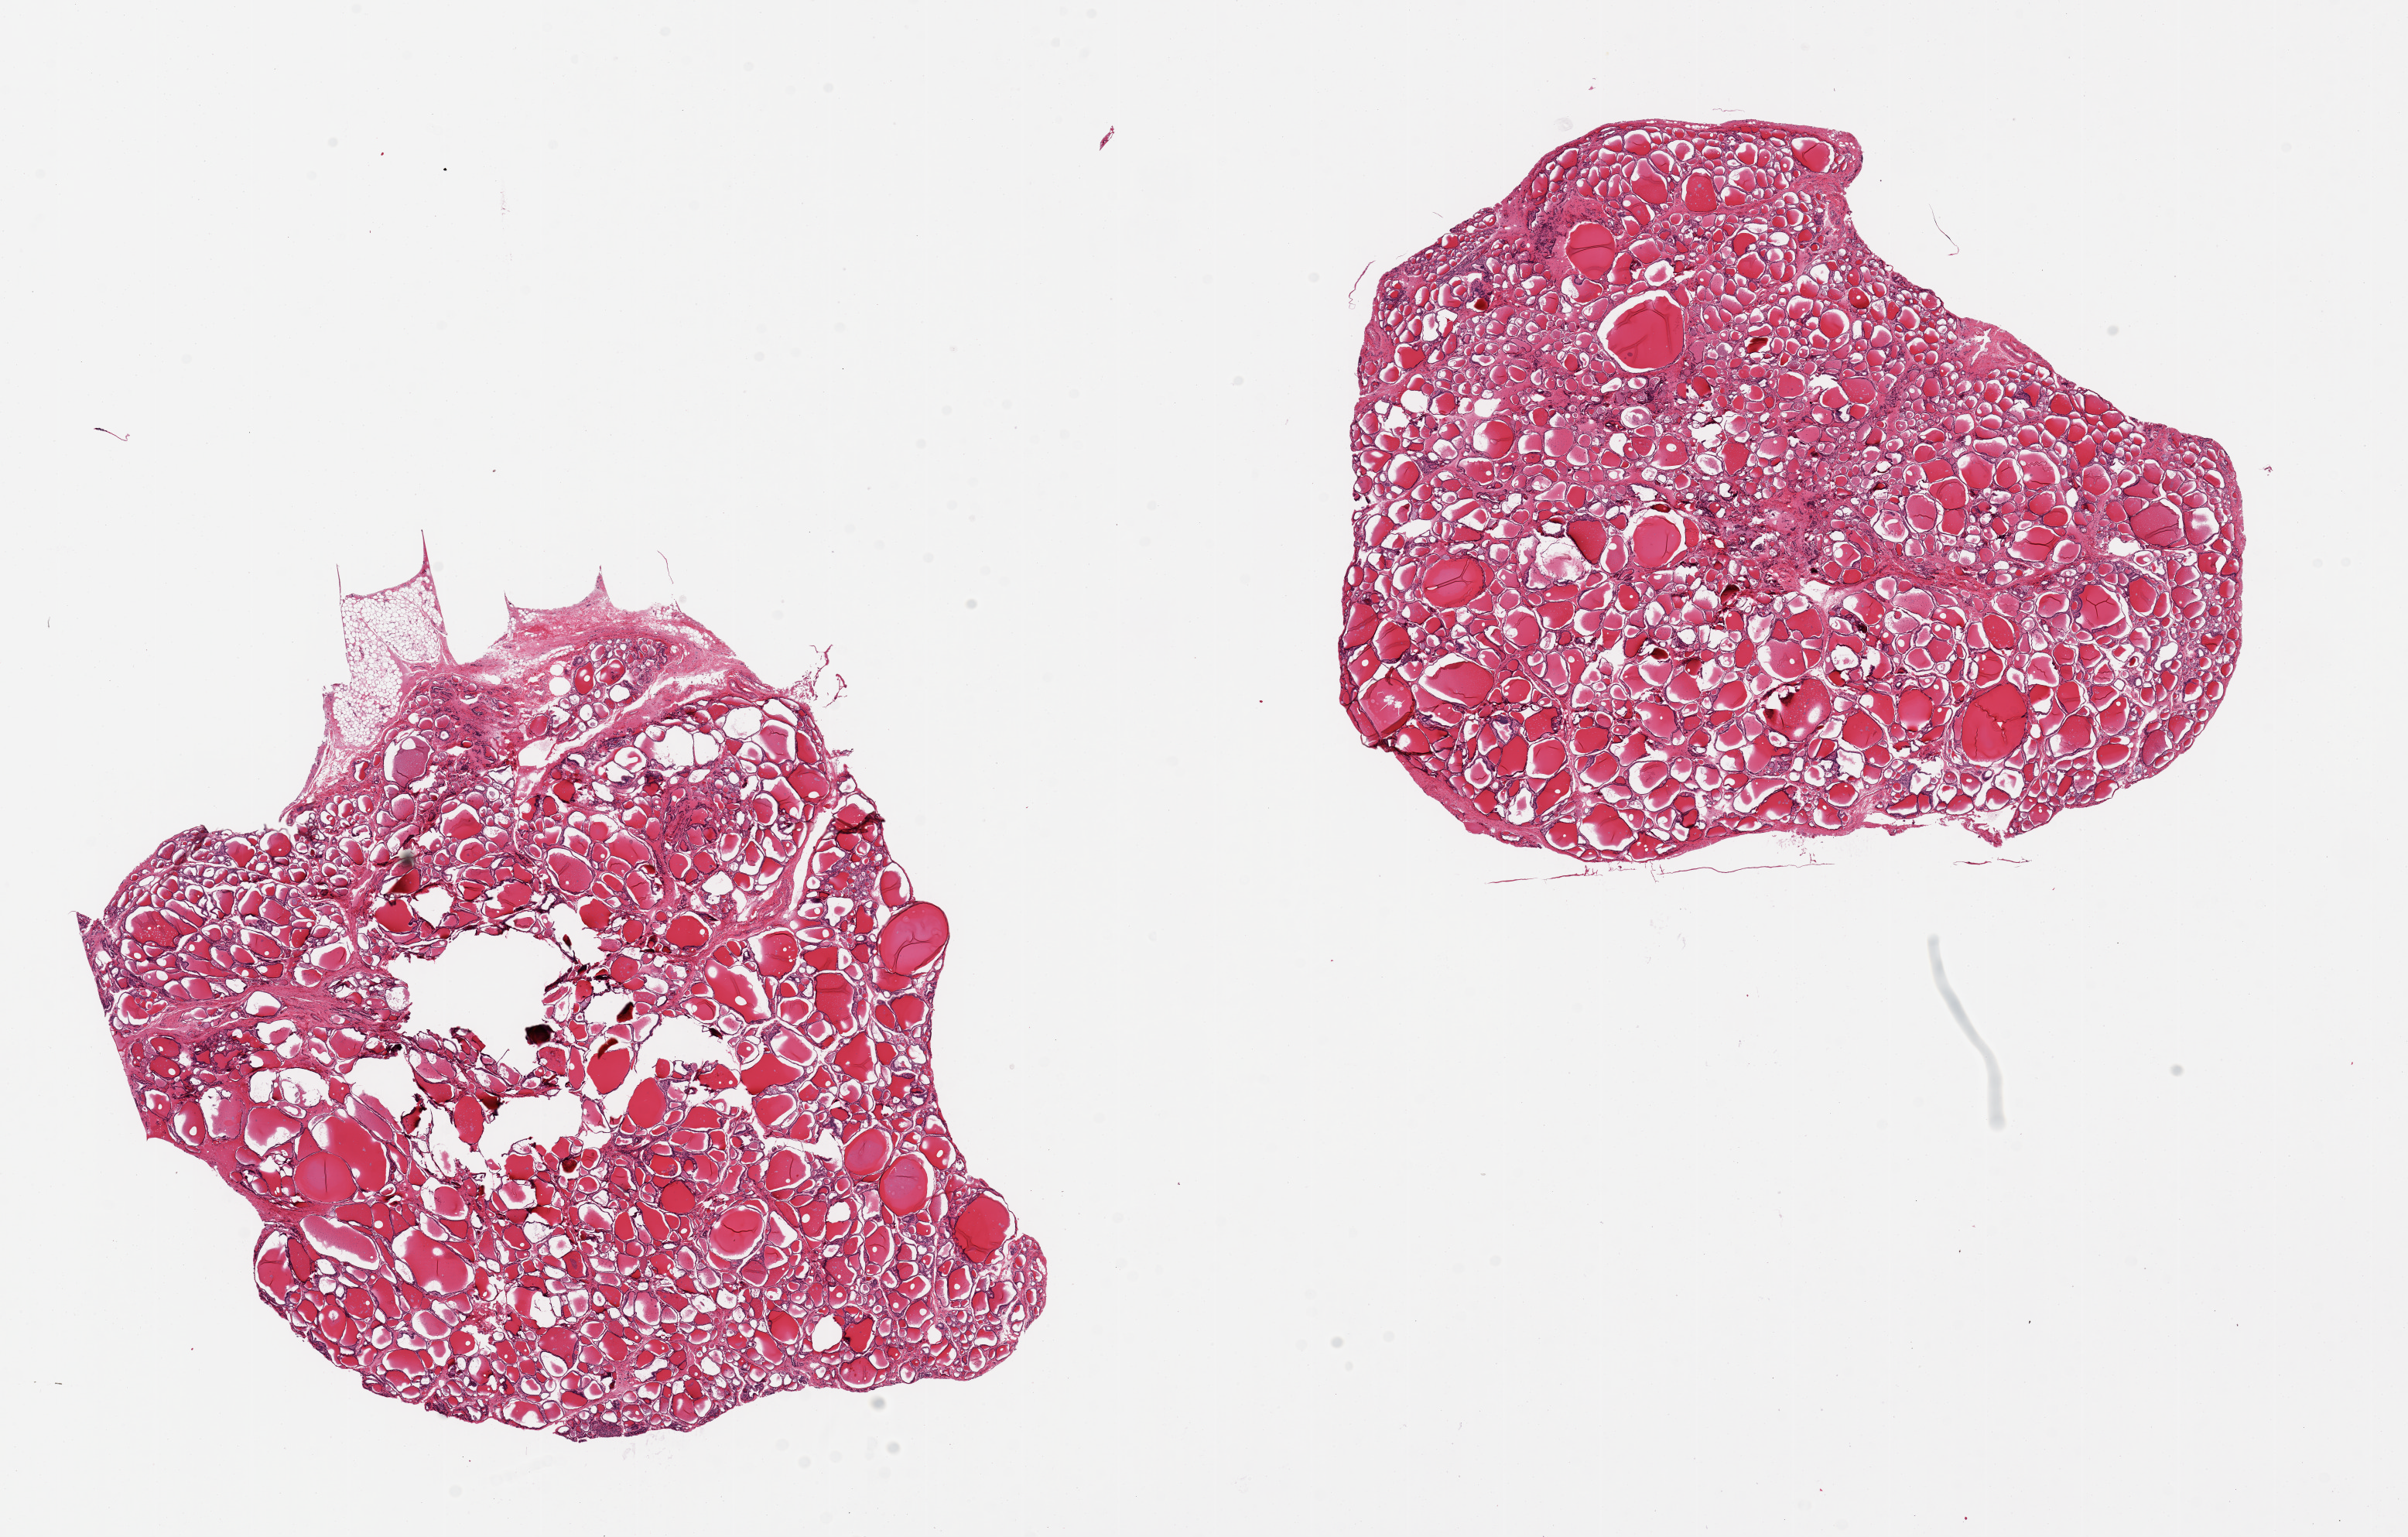
Hematoxylin and eosin (H&E) whole-slide image, a low-resolution overview of the entire scanned area, about 24.6 x 15.7 mm. PAXgene-fixed, paraffin-embedded tissue. Section of thyroid (target tissue). Tissue donor sample. Donor sex: female.
Review note (as recorded): 2 pieces, 10x9 & 10x8mm; fewe scarred areas.